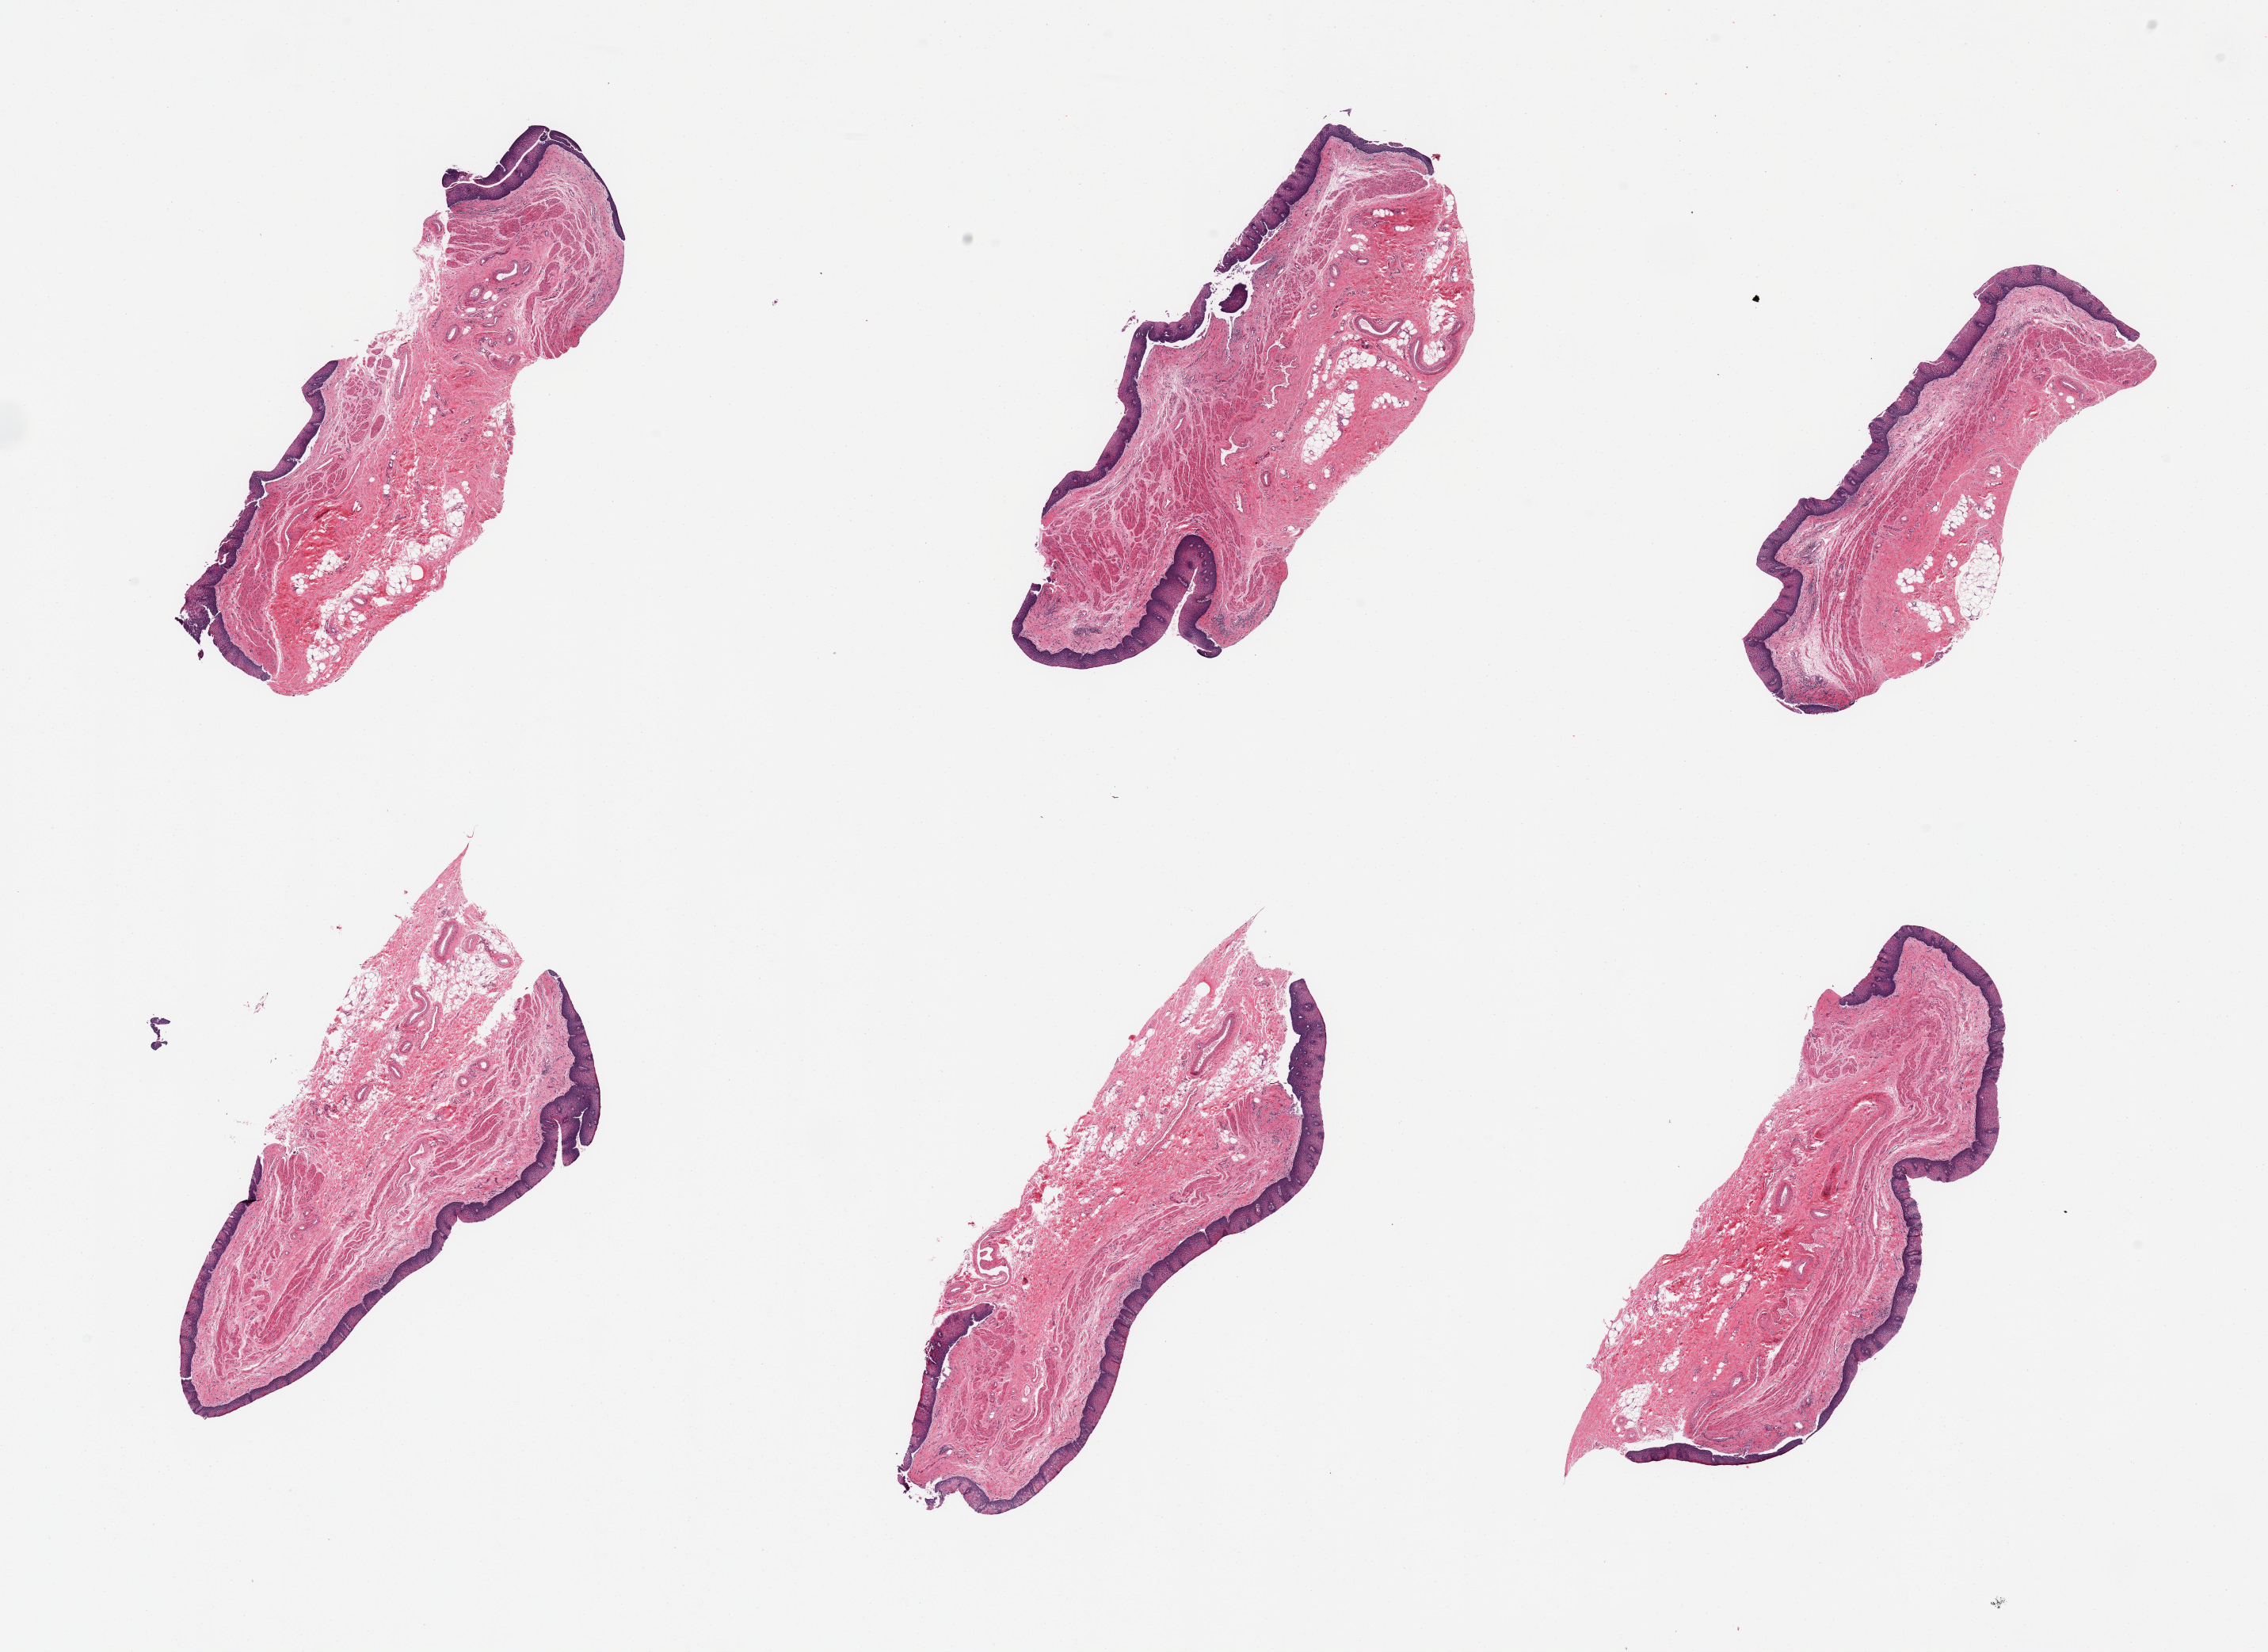
Digitized H&E-stained section, whole scanned area (about 22.6 x 16.5 mm, acquisition: 20x scan) shown as a low-resolution overview, PAXgene-fixed paraffin-embedded (PFPE) section, target tissue: esophageal mucous membrane, donor tissue sample. Donor: male.
Reviewer comment on this tissue sample: 6 pieces; up to 50% fibrovascular and fatty content in submucosal portion.